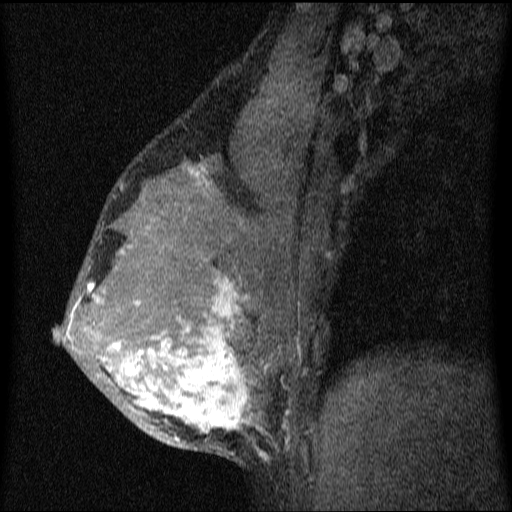
Breast MRI (dynamic contrast-enhanced), one sagittal slice. Slice 42 of 64 in the series (ordered by position). Dynamic contrast-enhanced series, image 2 of 4 at this slice position (ordered by acquisition). 1.5 T. TE 4.2 ms, TR 9.1 ms. 2 mm slice thickness. 512 × 512 image matrix. Female patient, age 33 years.
Outlined on this slice (semi-automatically segmented with operator editing):
- analysis volume of interest (the breast-tissue region the enhancement analysis was run in; not a lesion): bounding box (x1, y1, x2, y2) in pixels: (55, 151, 336, 458)
- tumour enhancement mask (voxels above the 70 % enhancement threshold inside the analysis volume of interest): (55, 167, 268, 457)